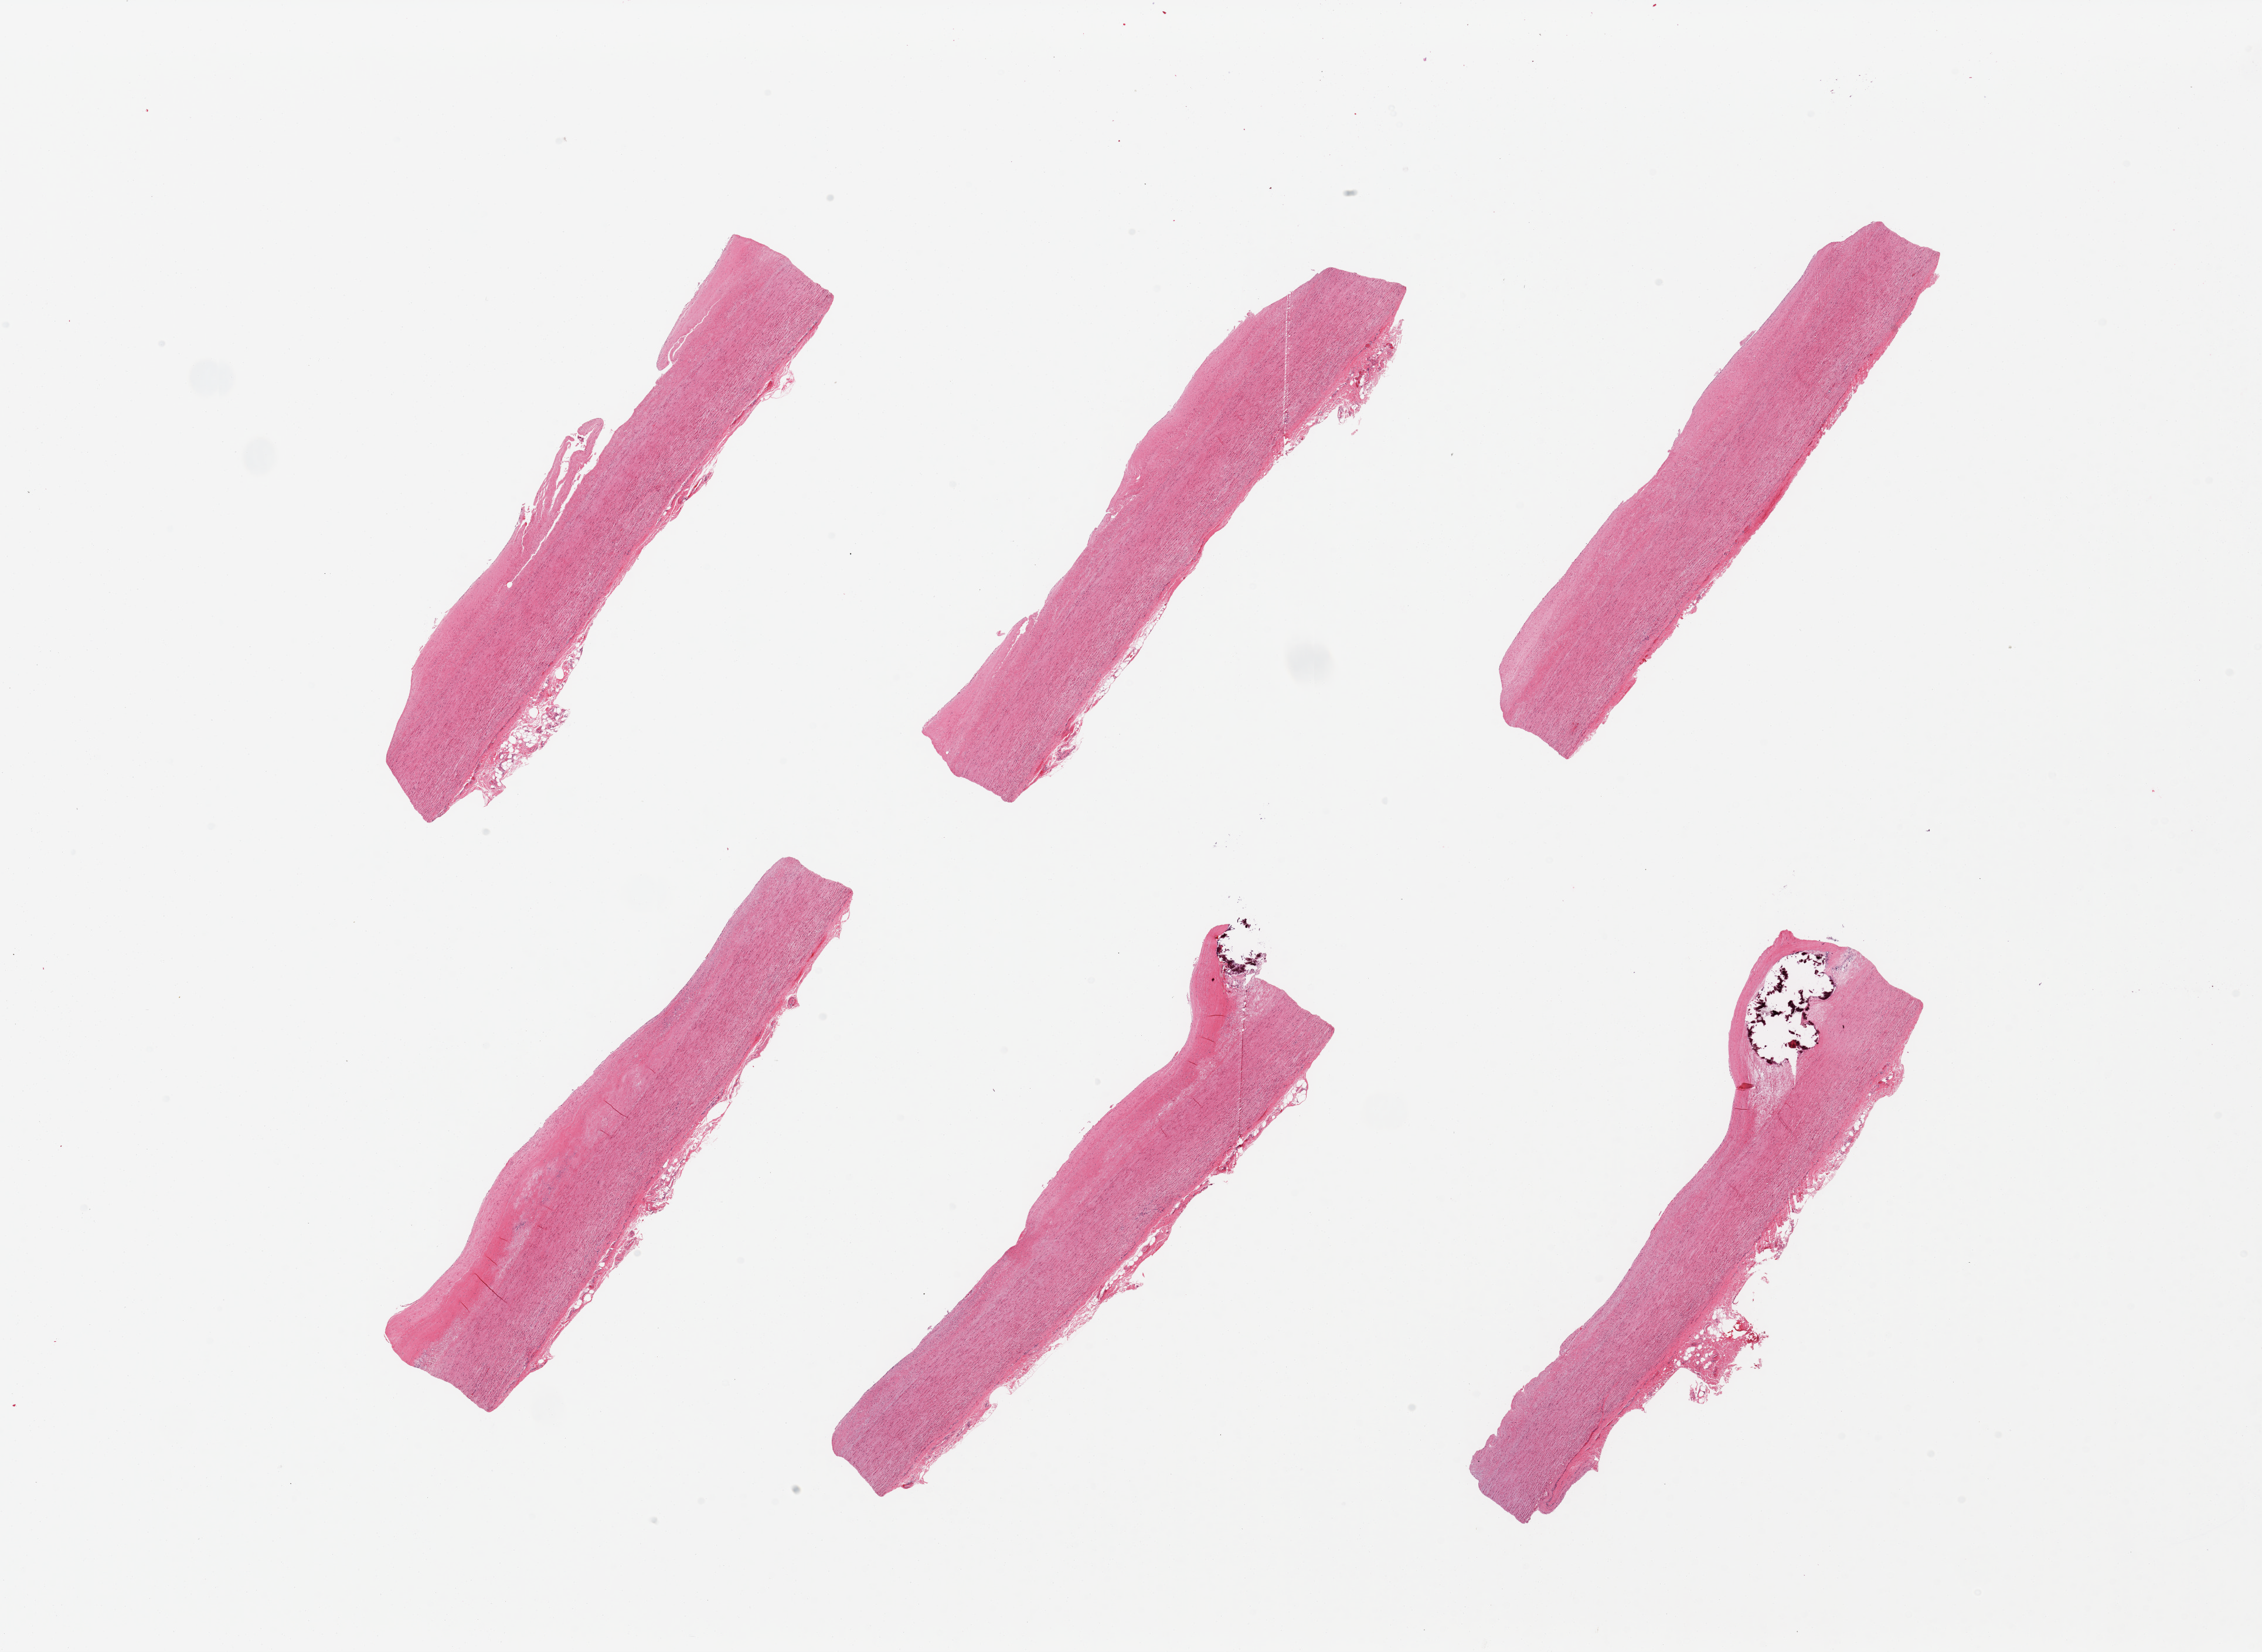
H&E whole-slide image — low-resolution overview of the scanned area, about 30.5 x 22.3 mm; PAXgene-fixed, paraffin-embedded tissue; section of aorta (target tissue); tissue donor sample. Donor sex: male.
Review note (as recorded): 6 pieces atherosis up to ~1.2mm, focally calcified.